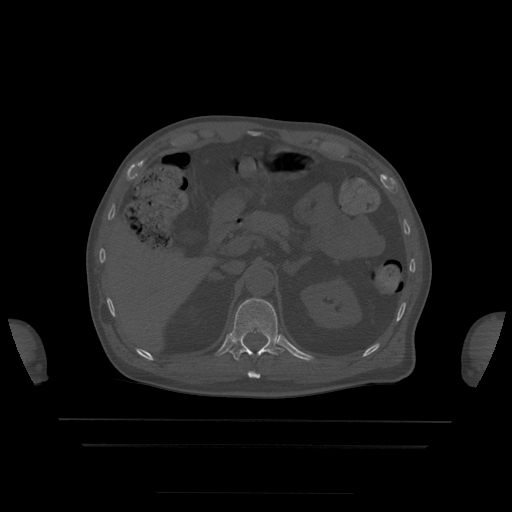
CT including the spine, one axial slice; slice 198 of 522 in the series (ordered by position); bone window (W 1800 / L 400 HU); 512 × 512 image matrix, field of view 436 × 436 mm. Patient age 68 years. From the clinical record (not read from this slice): primary cancer: urothelial.
Outlined on this slice (semi-automatic segmentation, software-assisted and operator-edited):
- T11 vertebra: bounding box (x1, y1, x2, y2) in pixels: (248, 372, 261, 379)
- T12 vertebra: (230, 298, 284, 361)